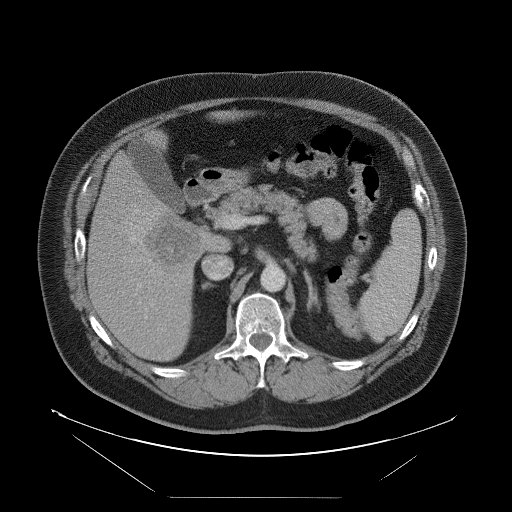
Contrast-enhanced abdominal CT, one axial slice. Position 51 of 114 along the scan axis. Intravenous contrast given. Soft-tissue window (W 400 / L 40 HU). 5 mm slice thickness. 512 × 512 image matrix, field of view 500 × 500 mm. Male patient, age 61 years. Case-level facts recorded for this patient, not image findings: diagnosis: colorectal cancer liver metastases, imaged before liver resection; multiple liver metastases: no; largest metastasis: 6.5 cm; disease in both lobes: yes.
Outlined on this slice (outlined manually by an expert reader):
- liver: bounding box (x1, y1, x2, y2) in pixels: (89, 115, 235, 361)
- planned liver remnant (the part of the liver to remain after resection): (148, 131, 167, 148)
- liver metastasis: (148, 214, 199, 271)